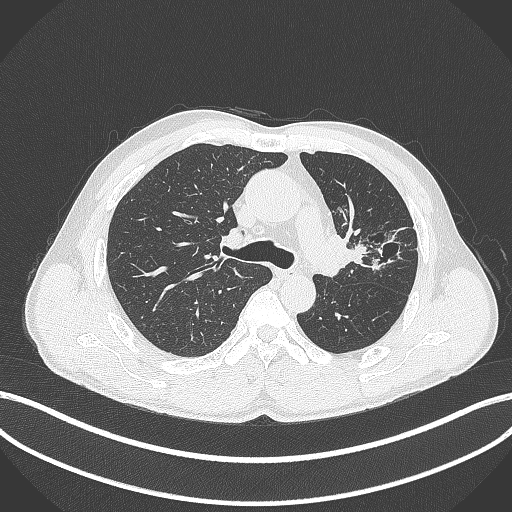
Chest CT, one axial slice; slice 274 of 429 in the series (ordered by position); 120 kVp; lung window (W 1500 / L -600 HU); 512 × 512 image matrix, field of view 400 × 400 mm. Male patient, age 57 years. Case-level facts recorded for this patient, not image findings: clinical TNM (as recorded): T2b N0 M0.
Annotated regions visible in this slice (bounding box drawn by a radiologist):
- lung tumour (recorded histology: squamous cell carcinoma): bounding box (x1, y1, x2, y2) in pixels: (328, 236, 371, 272)